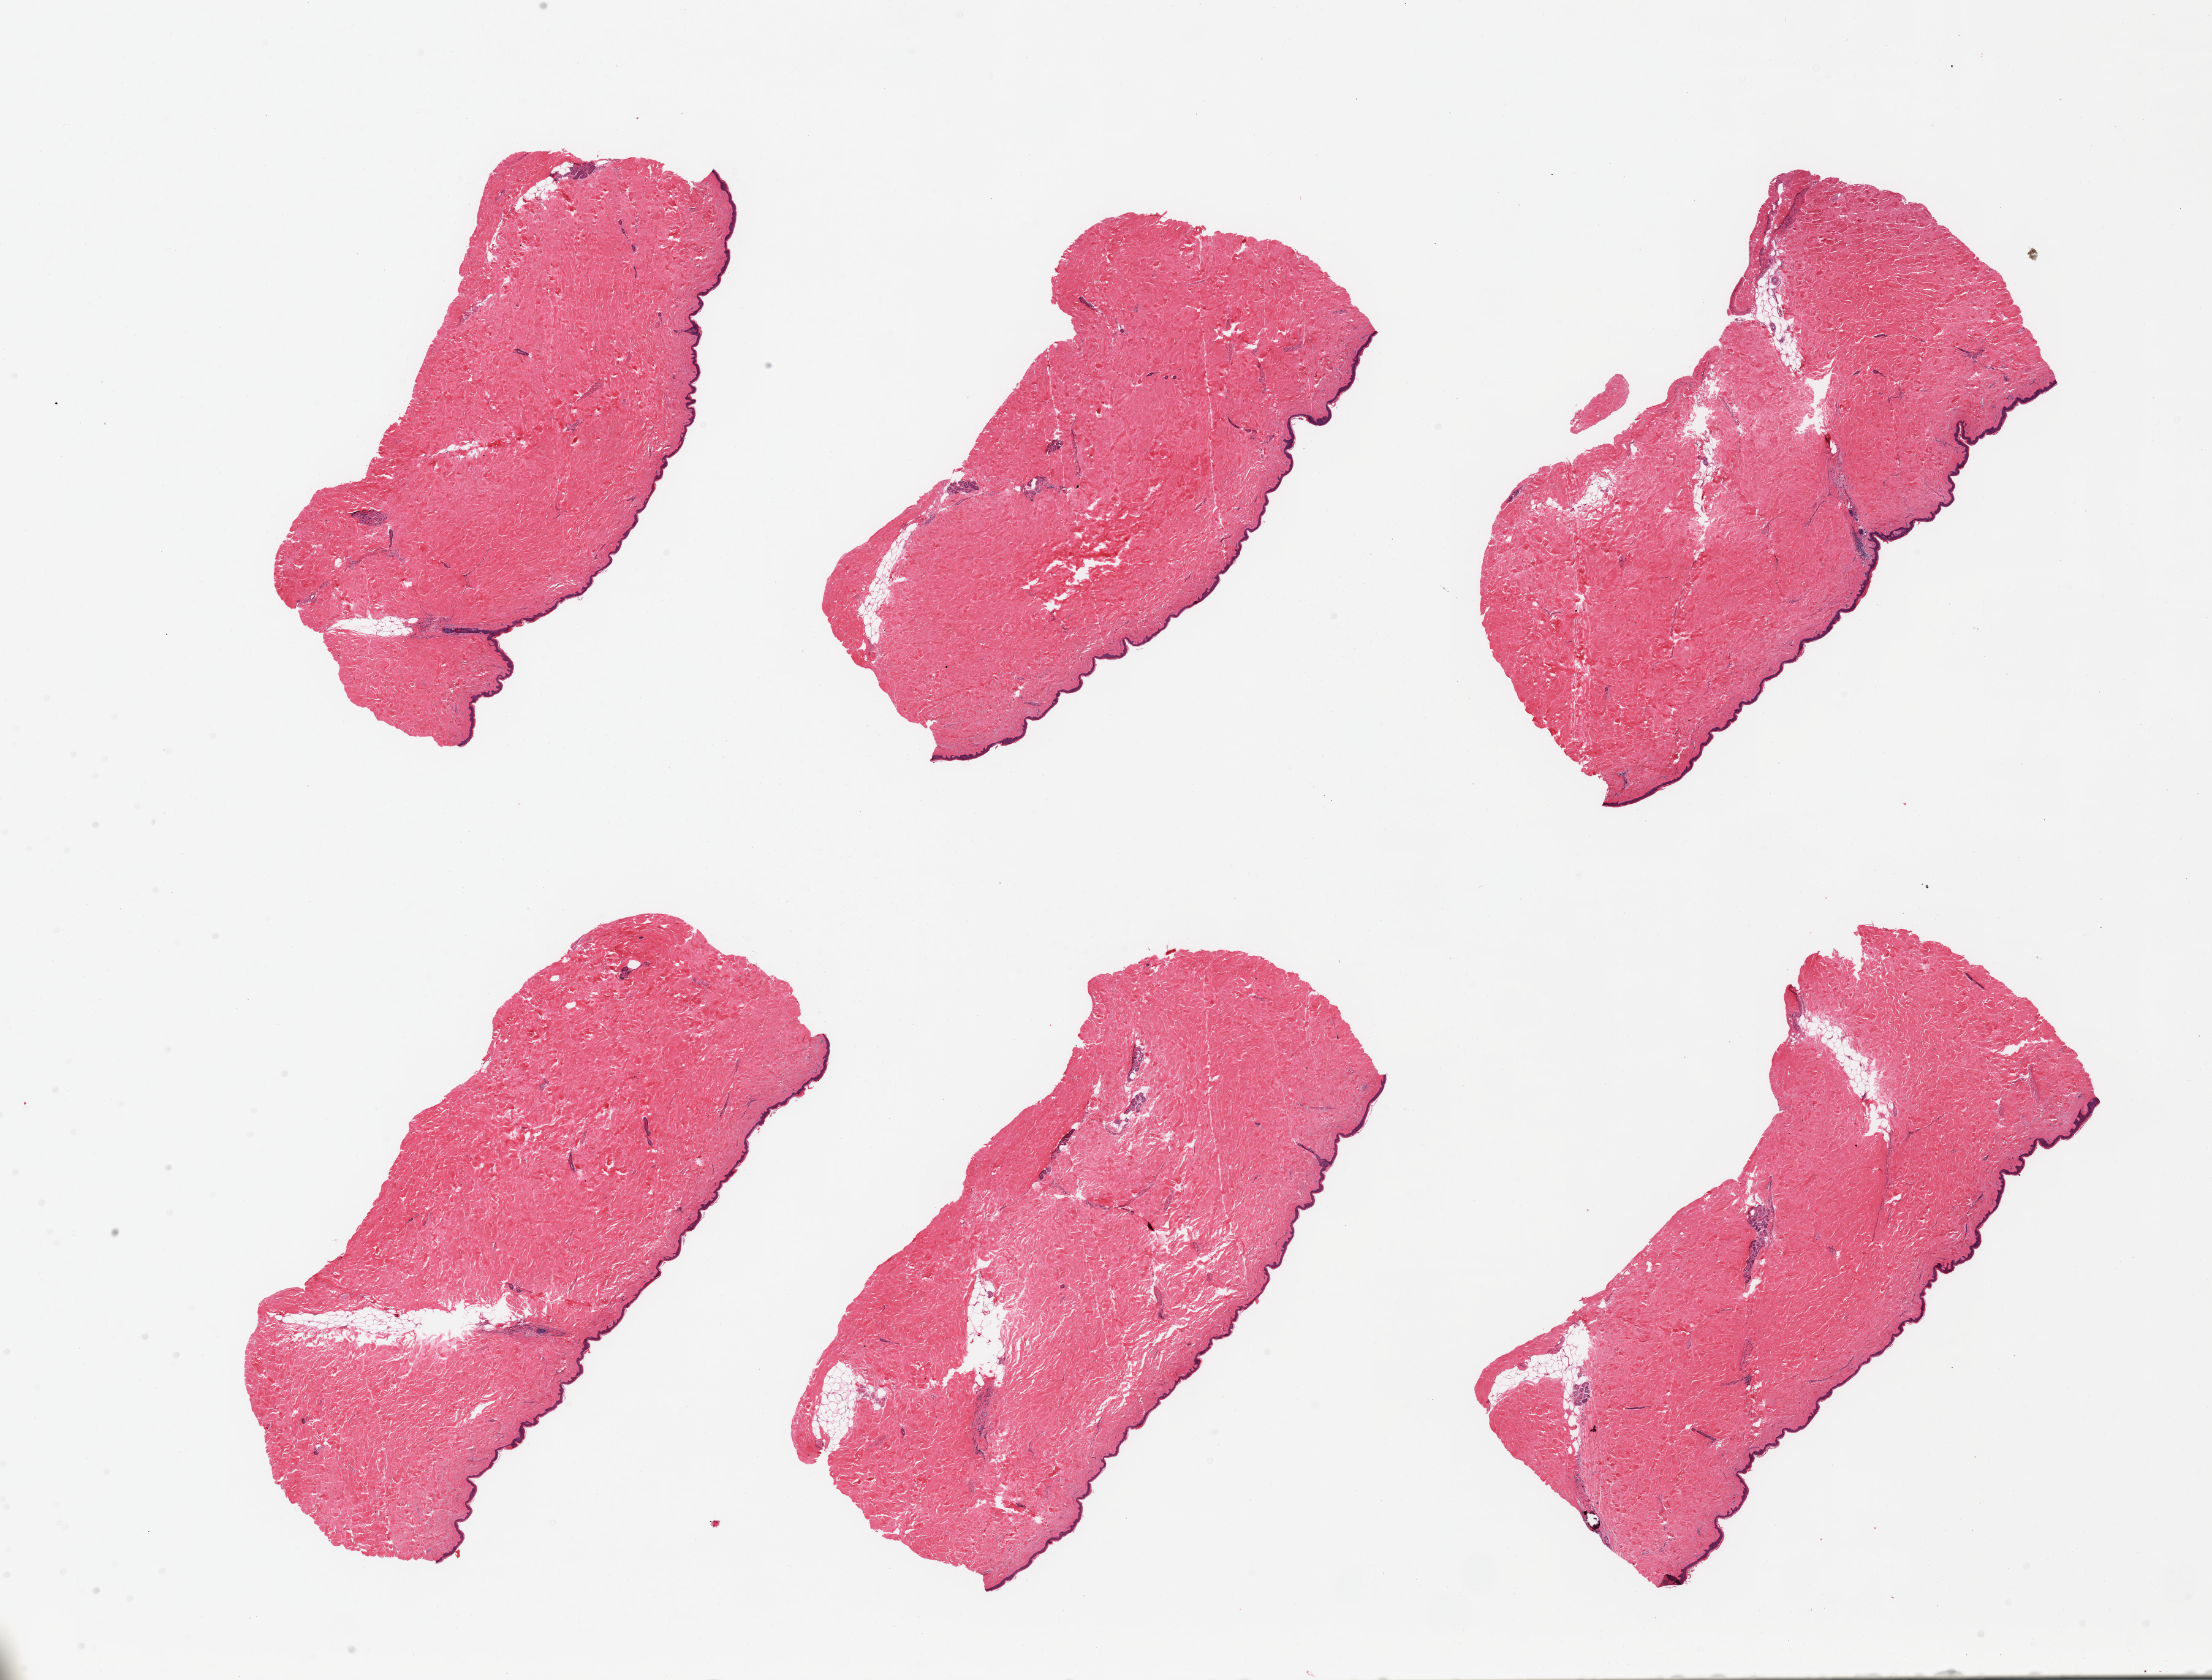
Digitized haematoxylin and eosin-stained section, shown as a low-resolution overview of the whole scanned area (about 28.5 x 21.7 mm); PAXgene-fixed, paraffin-embedded tissue; target tissue: skin of suprapubic region; donor tissue sample. Male donor.
* review note (as recorded): 6 pieces, minimal dermal fat; squamous epithelium is ~20-30 microns